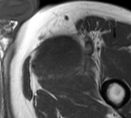
MRI of an extremity soft-tissue mass, one axial slice. Slice 53 of 55 in the series (ordered by position). MR volume resampled by the dataset authors to the PET/CT grid (not the native acquisition matrix). 3.27 mm slice thickness. 131 × 118 image matrix, field of view 128 × 115 mm. Male patient. From the clinical record (not read from this slice): histological type: pleiomorphic liposarcoma; grade: high; site of the primary tumour: left thigh.
Annotated regions visible in this slice (expert contour drawn on MRI and transferred to this co-registered scan by the dataset authors):
- gross tumour volume including surrounding oedema: bounding box <32,29,97,74> (left, top, right, bottom; pixels)
- gross tumour volume (mass): <32,34,74,65>